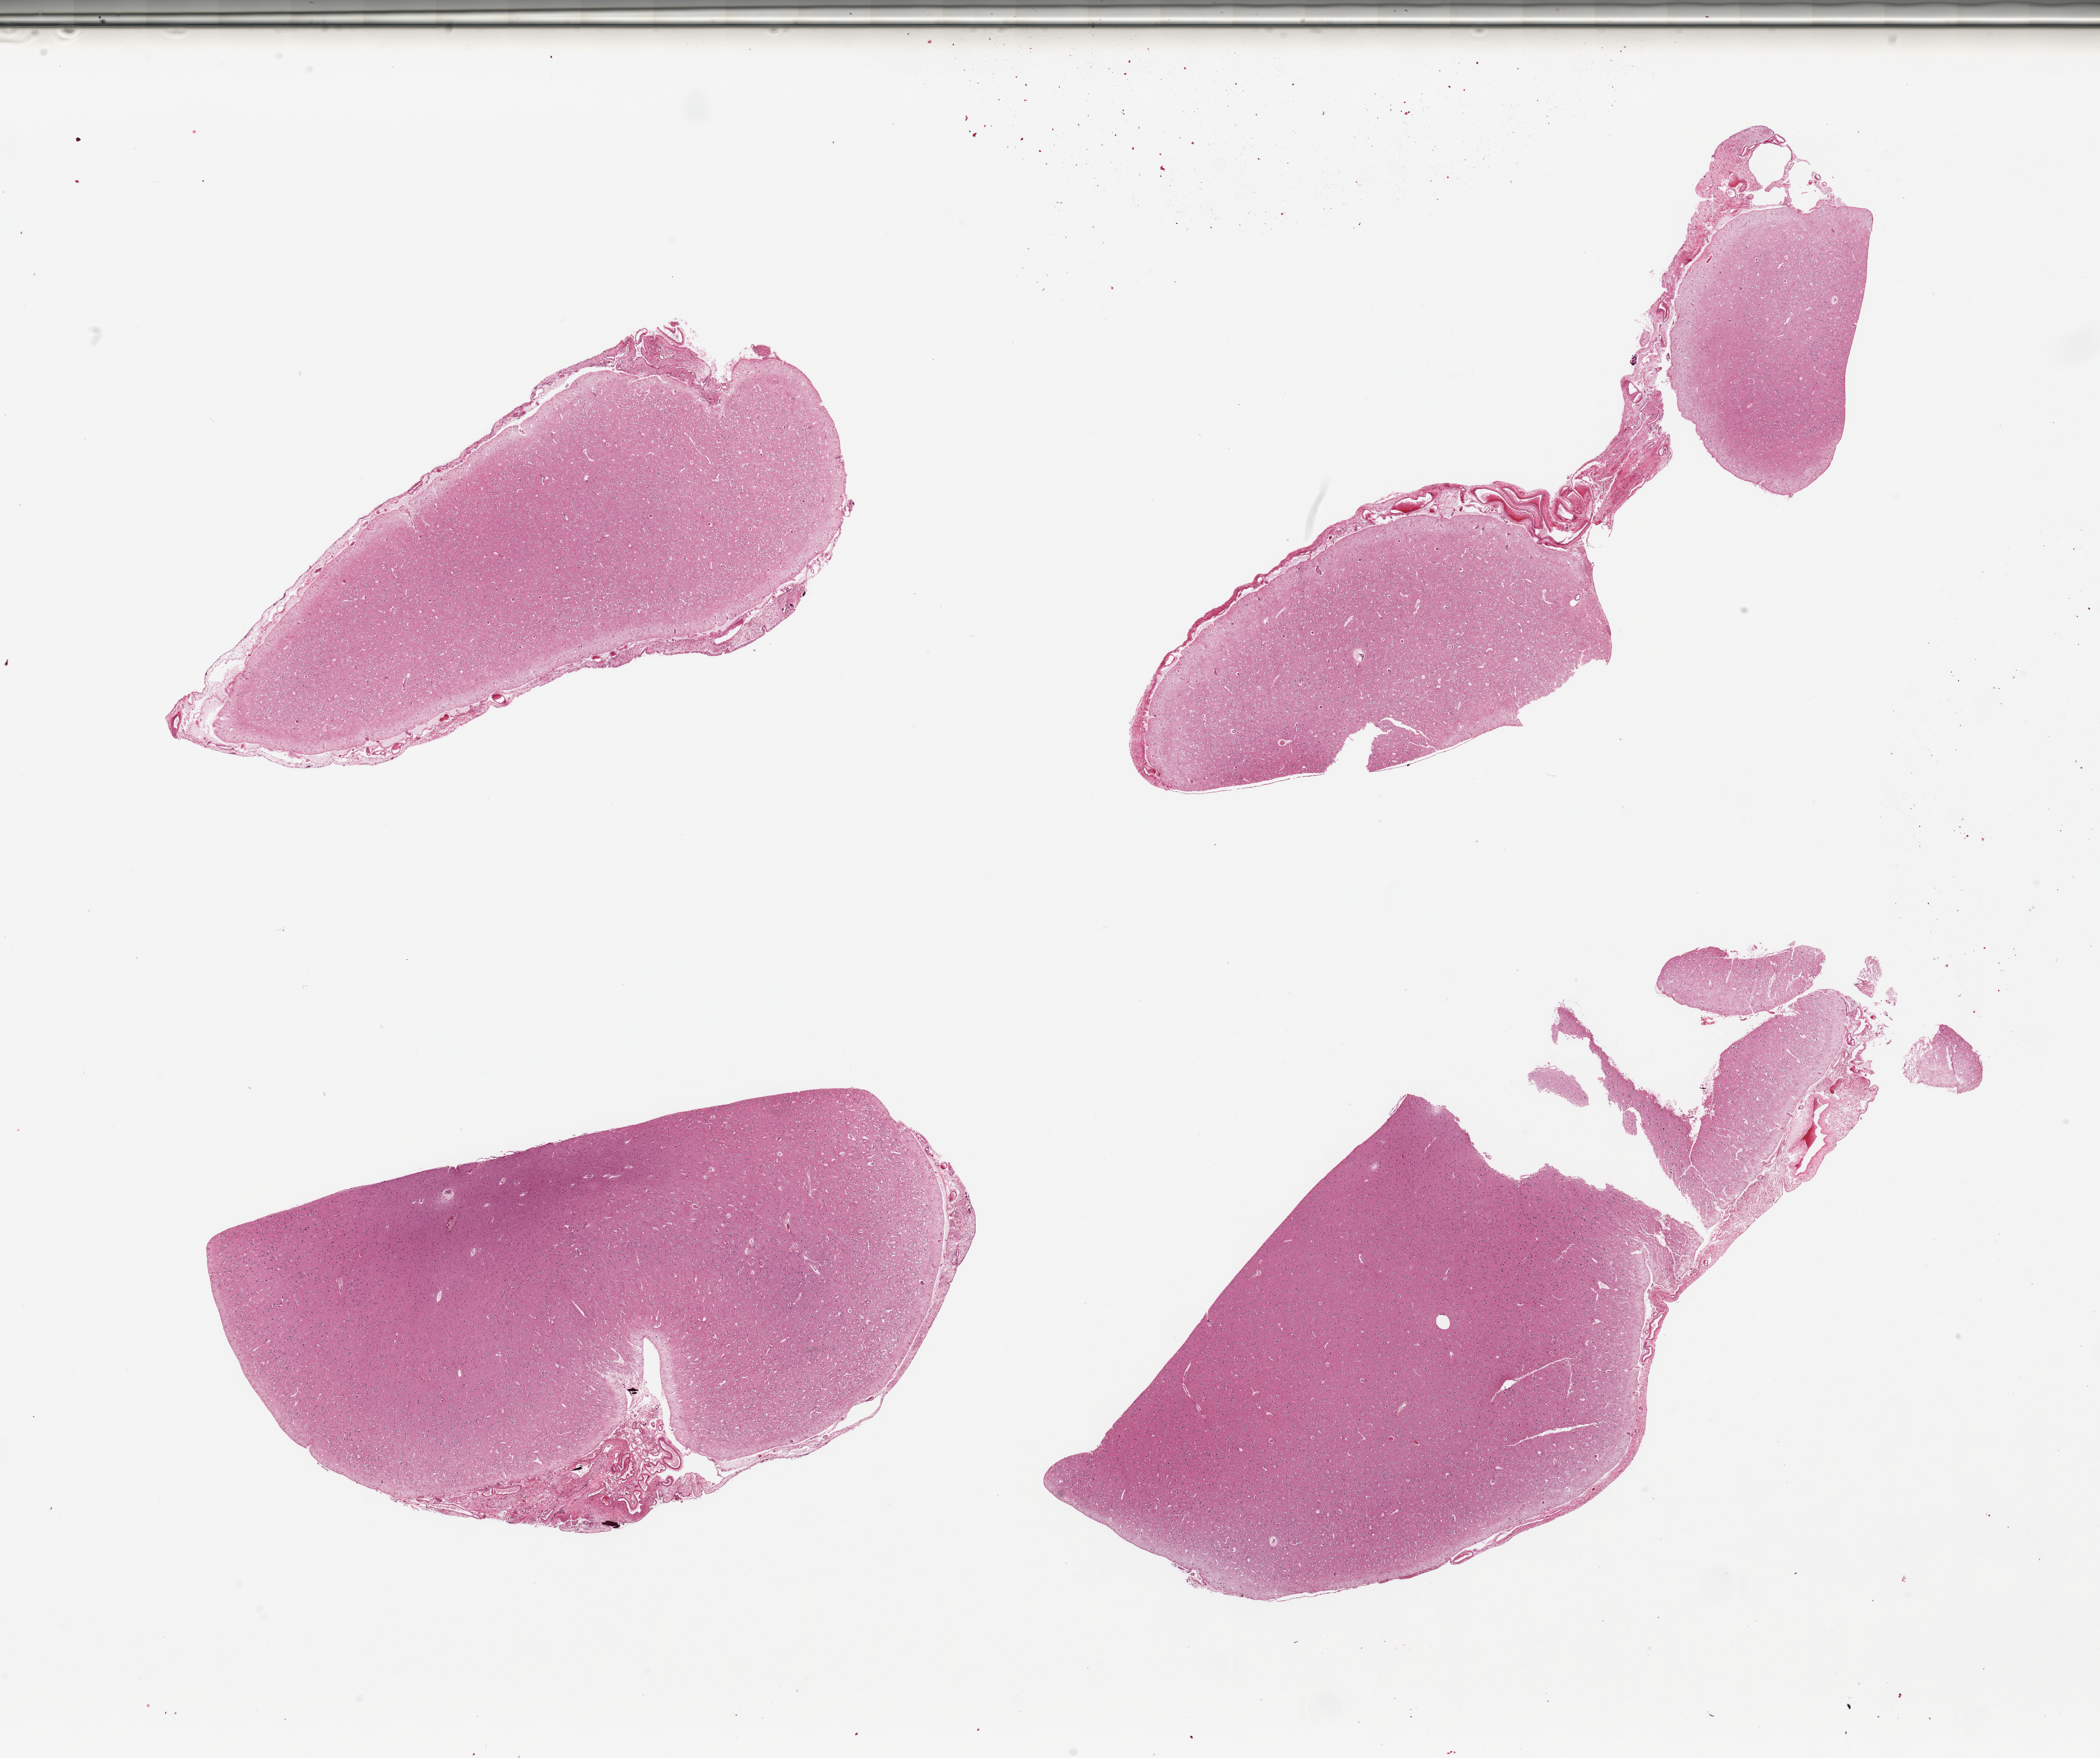
Digitized H&E-stained section, low-resolution overview of the scanned area, about 28.5 x 23.9 mm (from a 20x scan). PAXgene-fixed paraffin-embedded (PFPE) section. Target tissue: cerebral cortex. Tissue donor sample. Donor: male.
Review note (as recorded): 4 pieces, no abnormalities.